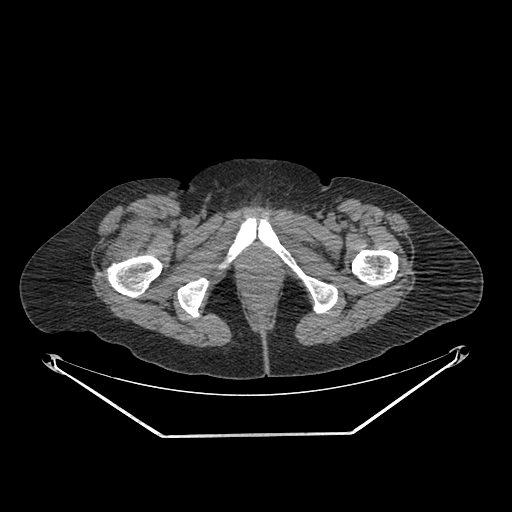
CT of an extremity soft-tissue mass (from a PET/CT study), one axial slice. Slice 284 of 311 in the series (ordered by position). Soft-tissue window (W 400 / L 40 HU). 3.75 mm slice thickness. 512 × 512 image matrix. Female patient. From the clinical record (not read from this slice): histological type: pleiomorphic undifferentiated sarcoma; grade: high; site of the primary tumour: right quadricep.
Annotated regions visible in this slice (expert contour drawn on MRI and transferred to this co-registered scan by the dataset authors):
- tumour plus oedema (research contour): bounding box <103,212,161,270> (left, top, right, bottom; pixels)